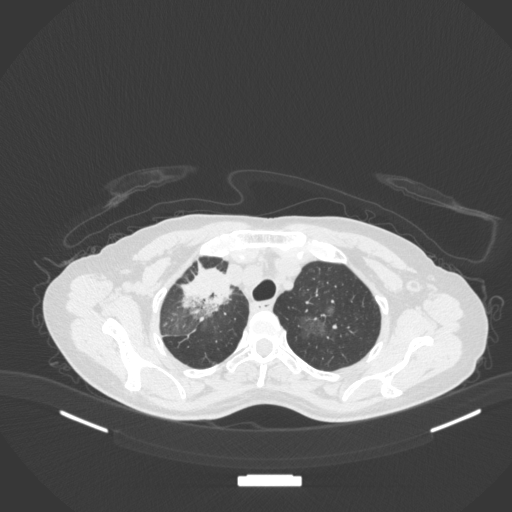
Chest CT, one axial slice; position 268 of 311 along the scan axis; reconstruction kernel B31f; lung window (W 1500 / L -600 HU); 1 mm slice thickness; 512 × 512 image matrix. Female patient, age 59 years. From the clinical record (not read from this slice): clinical TNM (as recorded): T3 N0 M0.
Outlined on this slice (bounding box drawn by a radiologist):
- lung tumour (recorded histology: adenocarcinoma): bounding box [x1, y1, x2, y2] px = [170, 254, 236, 324]